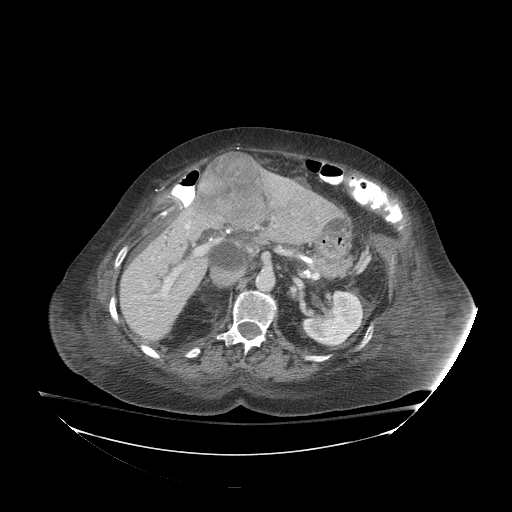
Contrast-enhanced abdominal CT (liver protocol), one axial slice; position 44 of 81 along the scan axis; 140 kVp; soft-tissue window (W 400 / L 40 HU); 2.5 mm slice thickness; 512 × 512 image matrix. From the clinical record (not read from this slice): diagnosis: hepatocellular carcinoma (patient treated with transarterial chemoembolisation; whether this scan precedes or follows treatment is not stated here); TNM stage (as recorded): Stage-I; Child-Pugh class: B; tumour differentiation: well-moderately differentiated; tumour nodularity: uninodular.
Annotated regions visible in this slice (semi-automatically segmented with operator editing):
- liver parenchyma outside the tumour (the mass and vessels are separate outlines, so this box may not span the whole liver): bounding box (x1, y1, x2, y2) in pixels: (120, 186, 340, 340)
- mass: (199, 153, 269, 227)
- liver vessels: (154, 222, 190, 297)